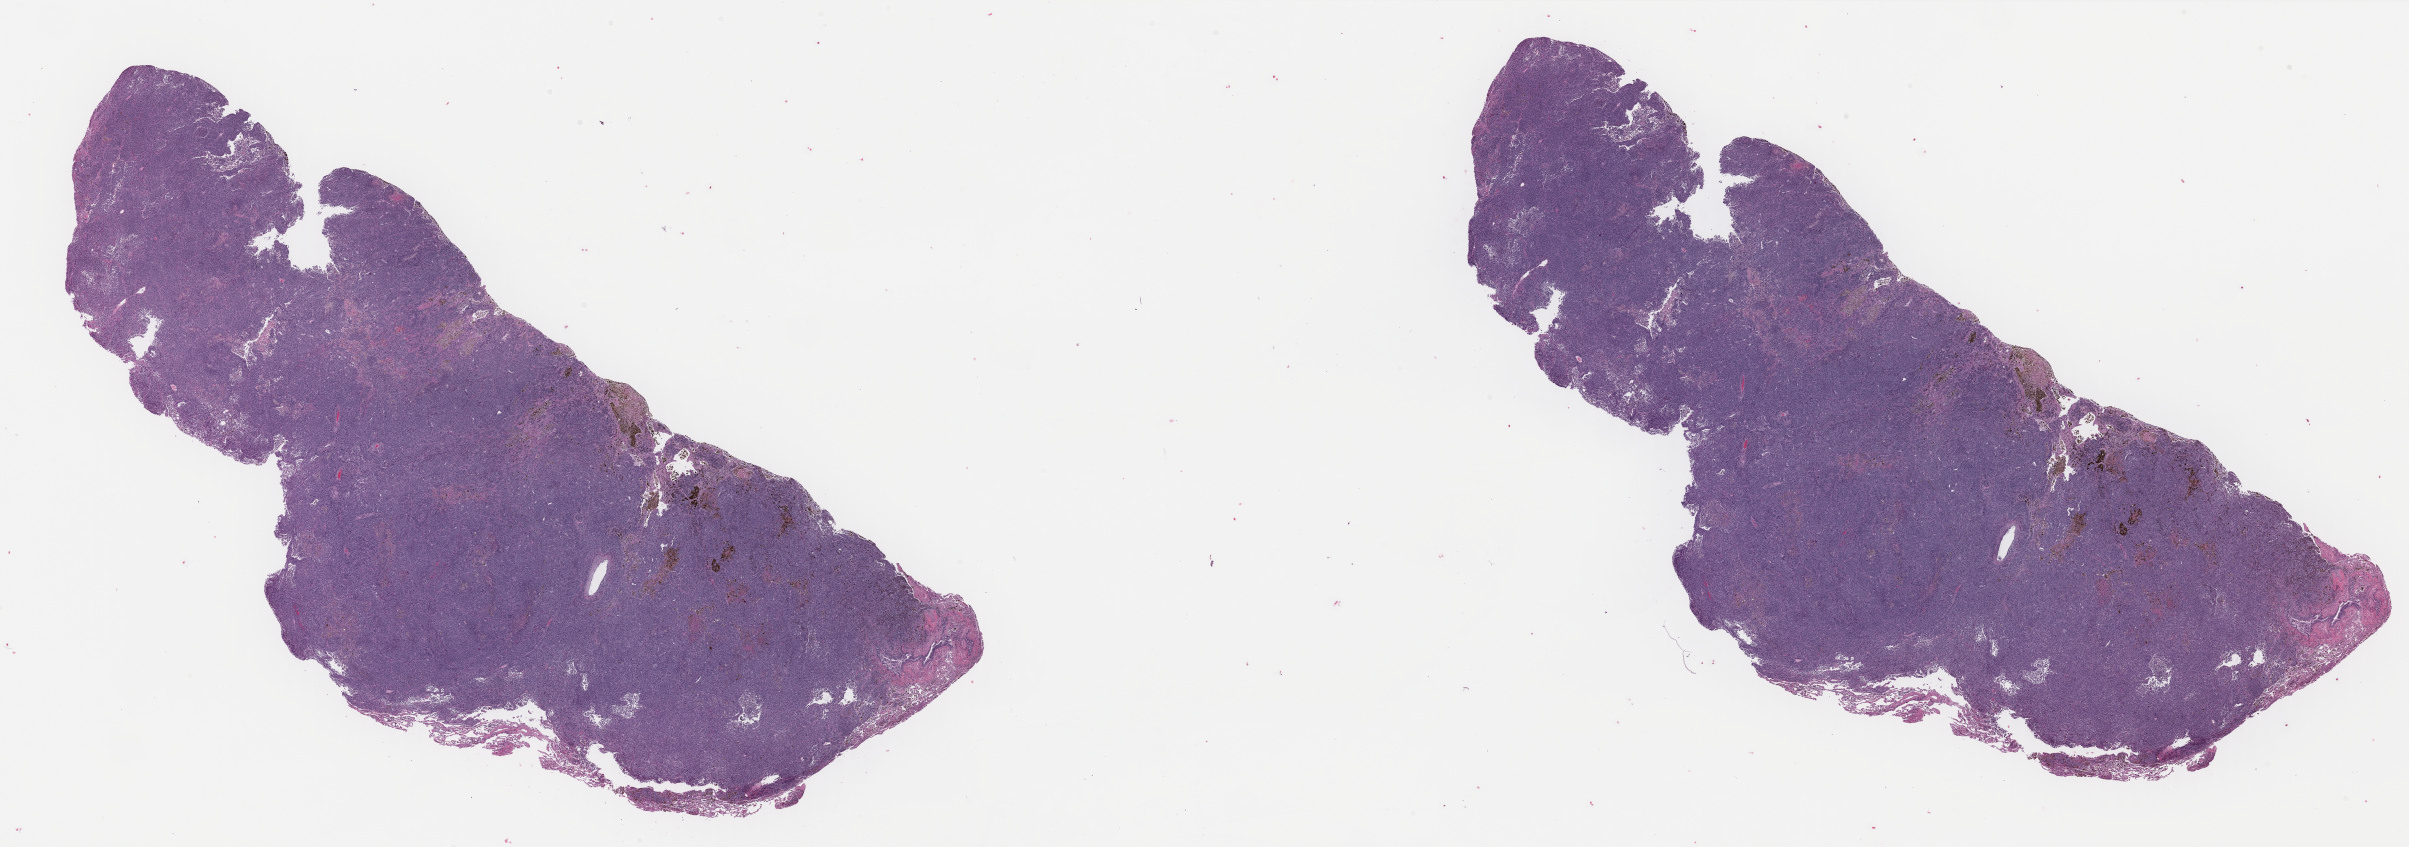
Whole-slide histology image, H&E-stained, a low-resolution overview of the entire scanned area, about 38.1 x 13.4 mm (slide scanned at 40x), formalin-fixed paraffin-embedded (FFPE) diagnostic section, metastatic tumour sample, sampled site: lower lobe, lung. Female, age 56 years at initial diagnosis.
• this section: metastatic tumour tissue
• patient diagnosis: Malignant melanoma, NOS